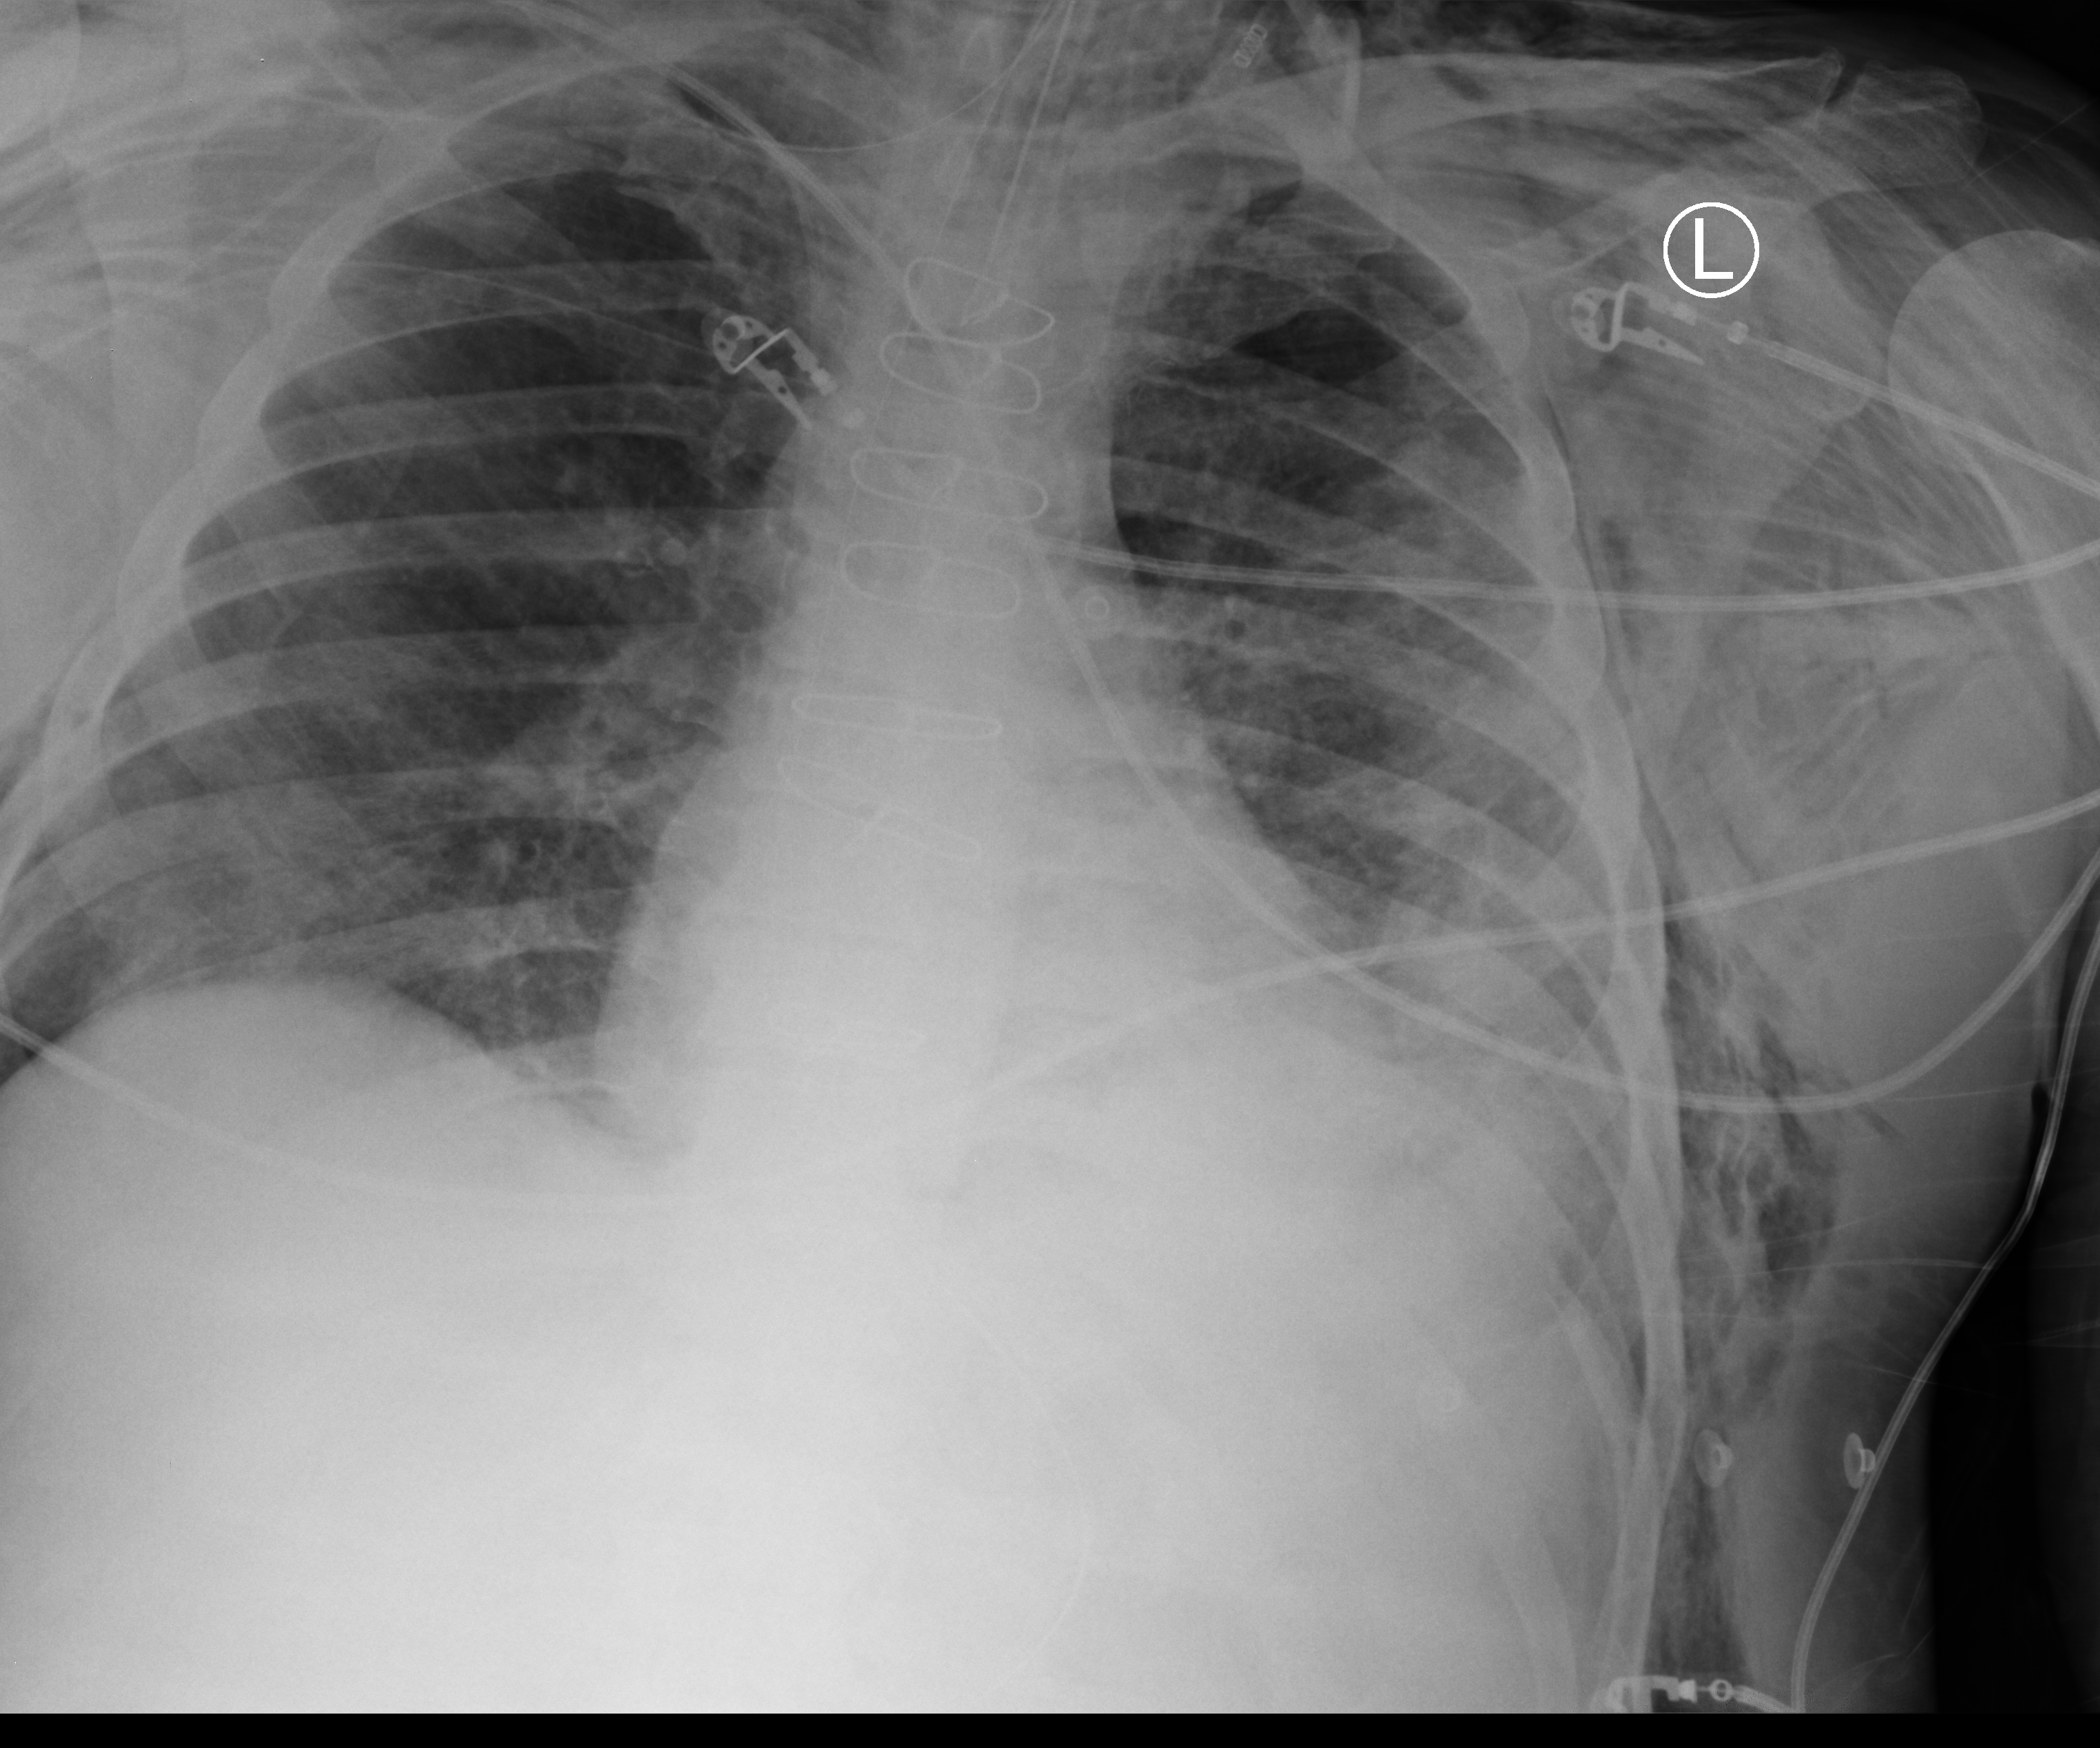
Chest X-ray (portable). Patient hospitalised with COVID-19; male, aged 60–74 years.
Admission-level facts for this patient (not findings on this image; timing relative to this image not recorded): admitted to intensive care during this hospital stay: yes.